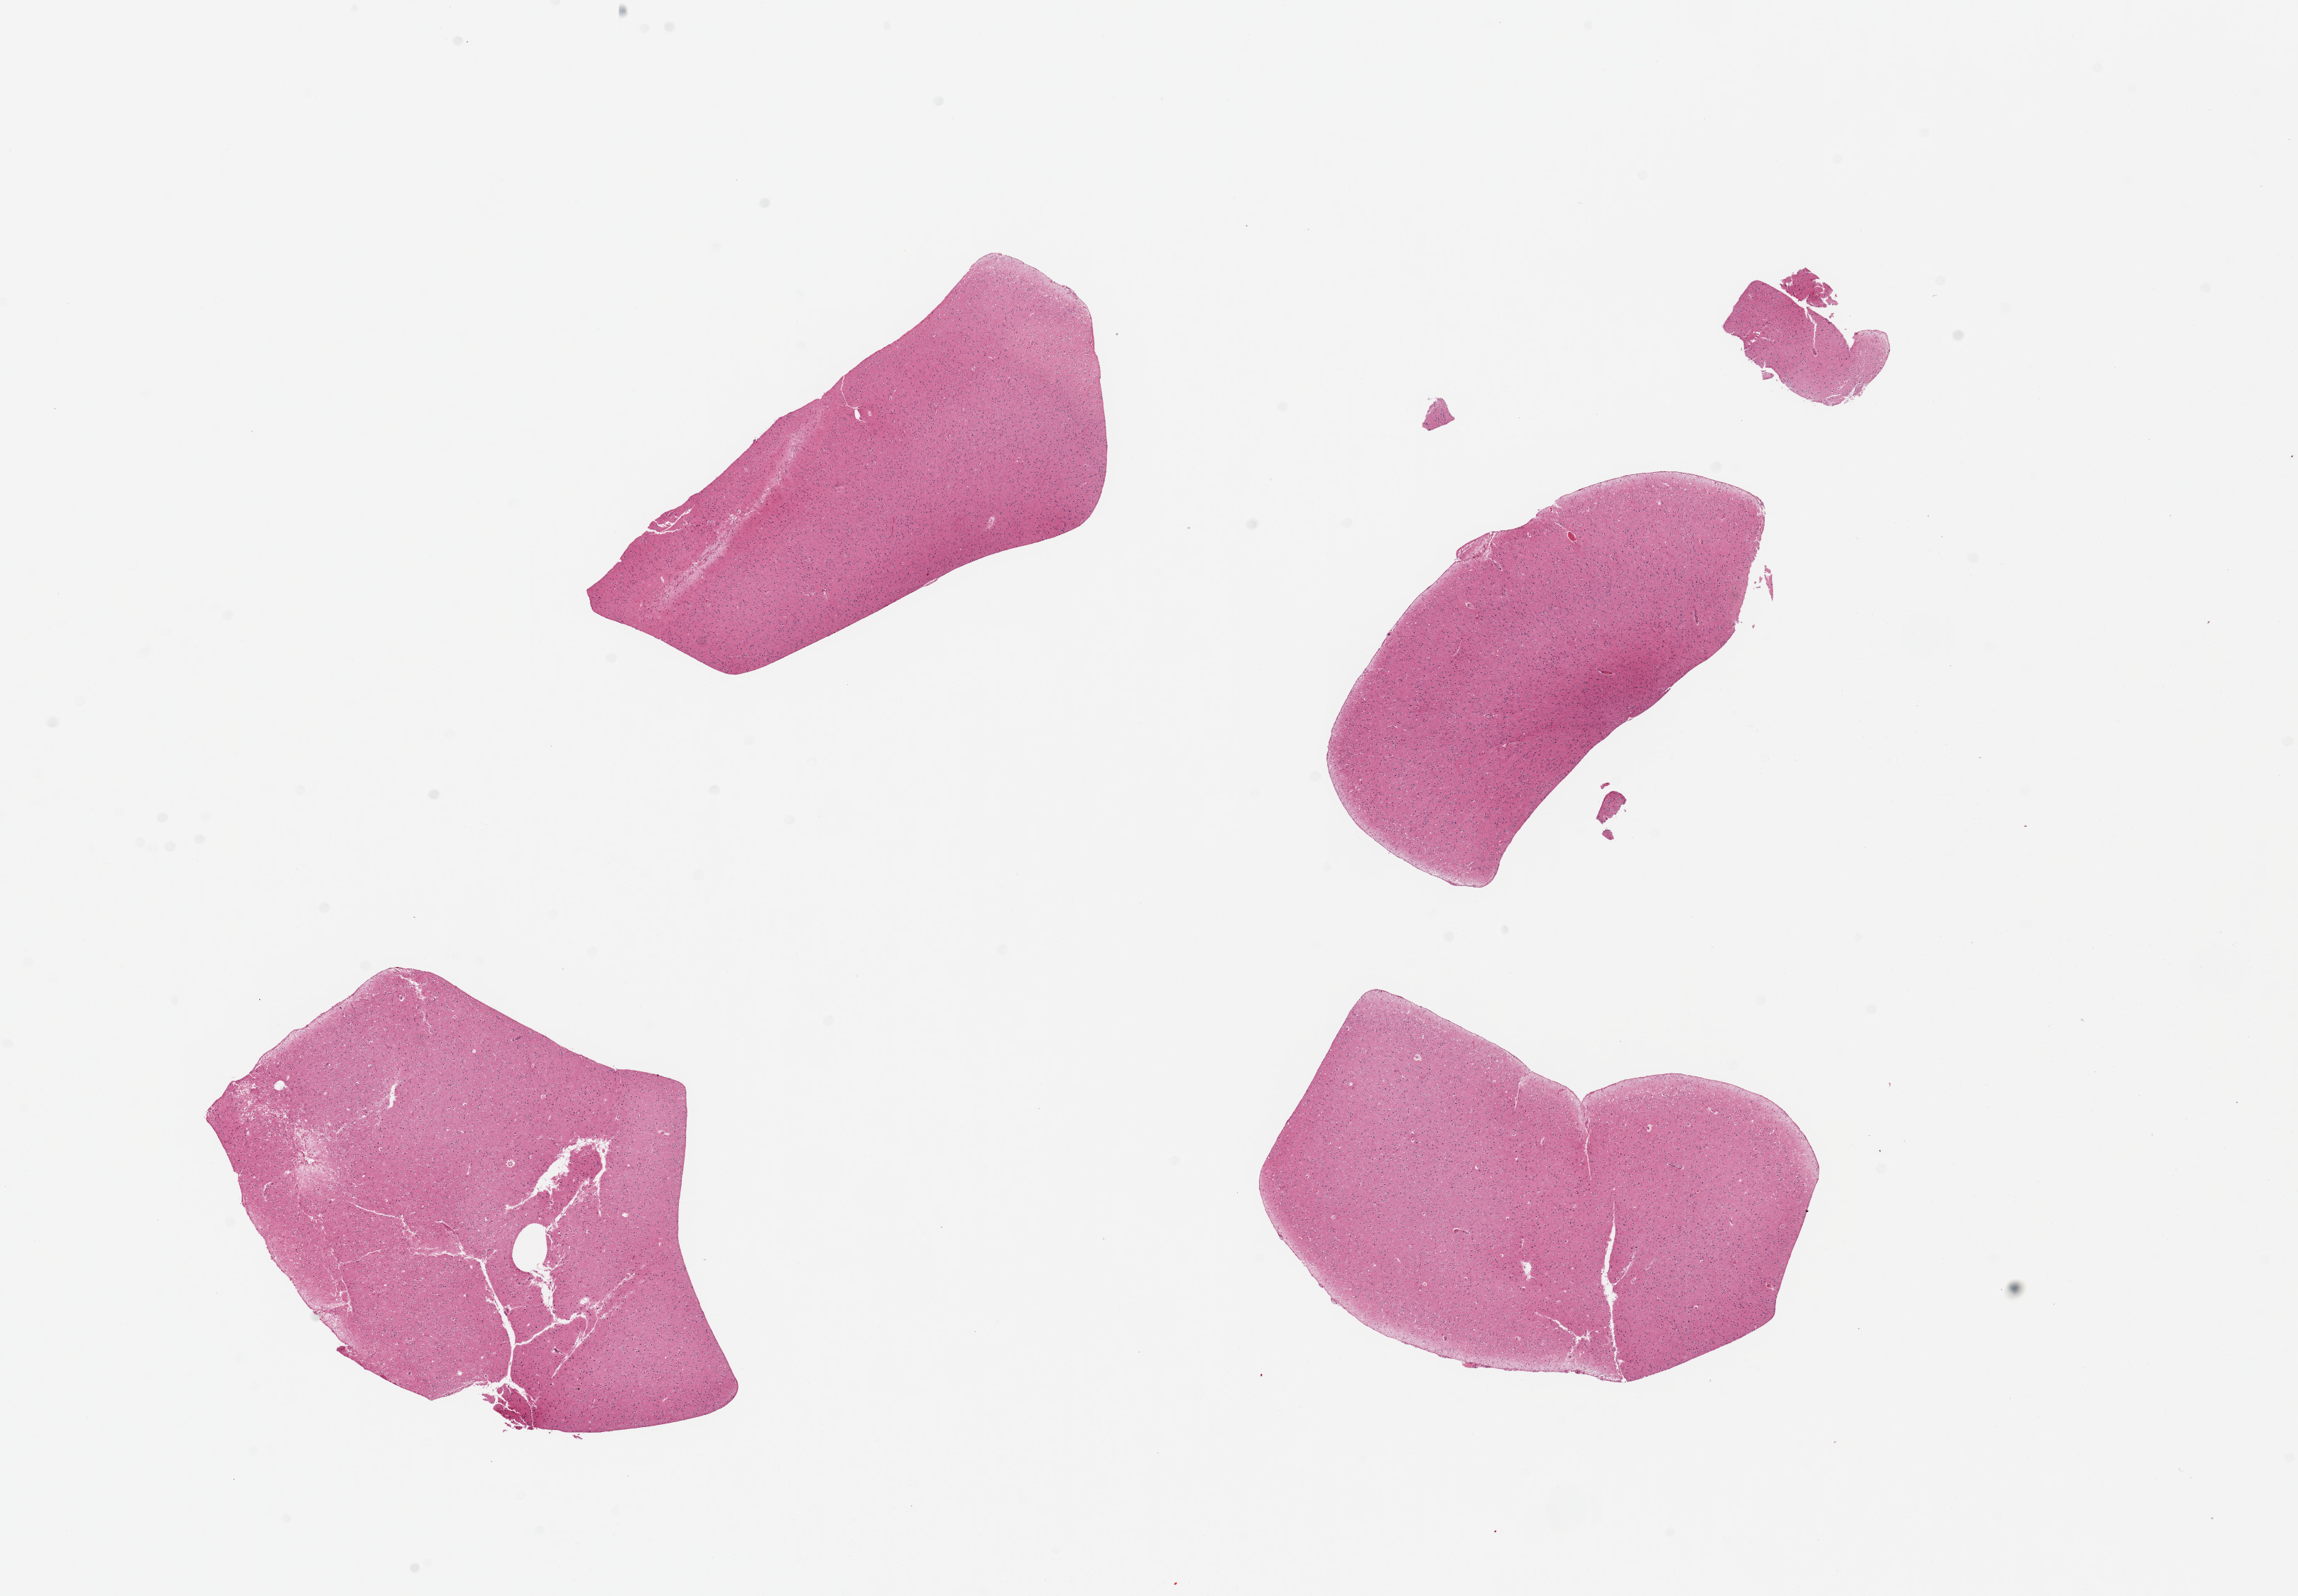
Digitized haematoxylin and eosin-stained section — low-resolution overview of the scanned area, about 25.6 x 17.8 mm; PAXgene-fixed paraffin-embedded (PFPE) section; section of cerebral cortex (target tissue); tissue donor sample. Female donor.
• review note (as recorded): 4 pieces